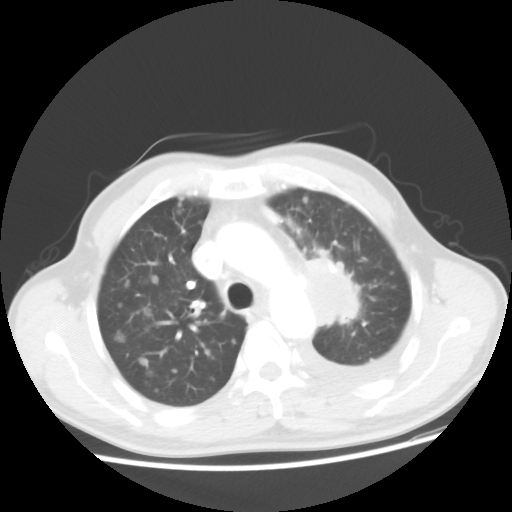
Chest CT, one axial slice; slice 34 of 48 in the series (ordered by position); 100 kVp; lung window (W 1500 / L -600 HU); 512 × 512 image matrix, field of view 362 × 362 mm. Male patient, age 55 years. From the clinical record (not read from this slice): clinical TNM (as recorded): T2 N3 M1a.
Annotated regions visible in this slice (bounding box drawn by a radiologist):
- lung tumour (recorded histology: squamous cell carcinoma): bounding box <305,256,362,339> (left, top, right, bottom; pixels)